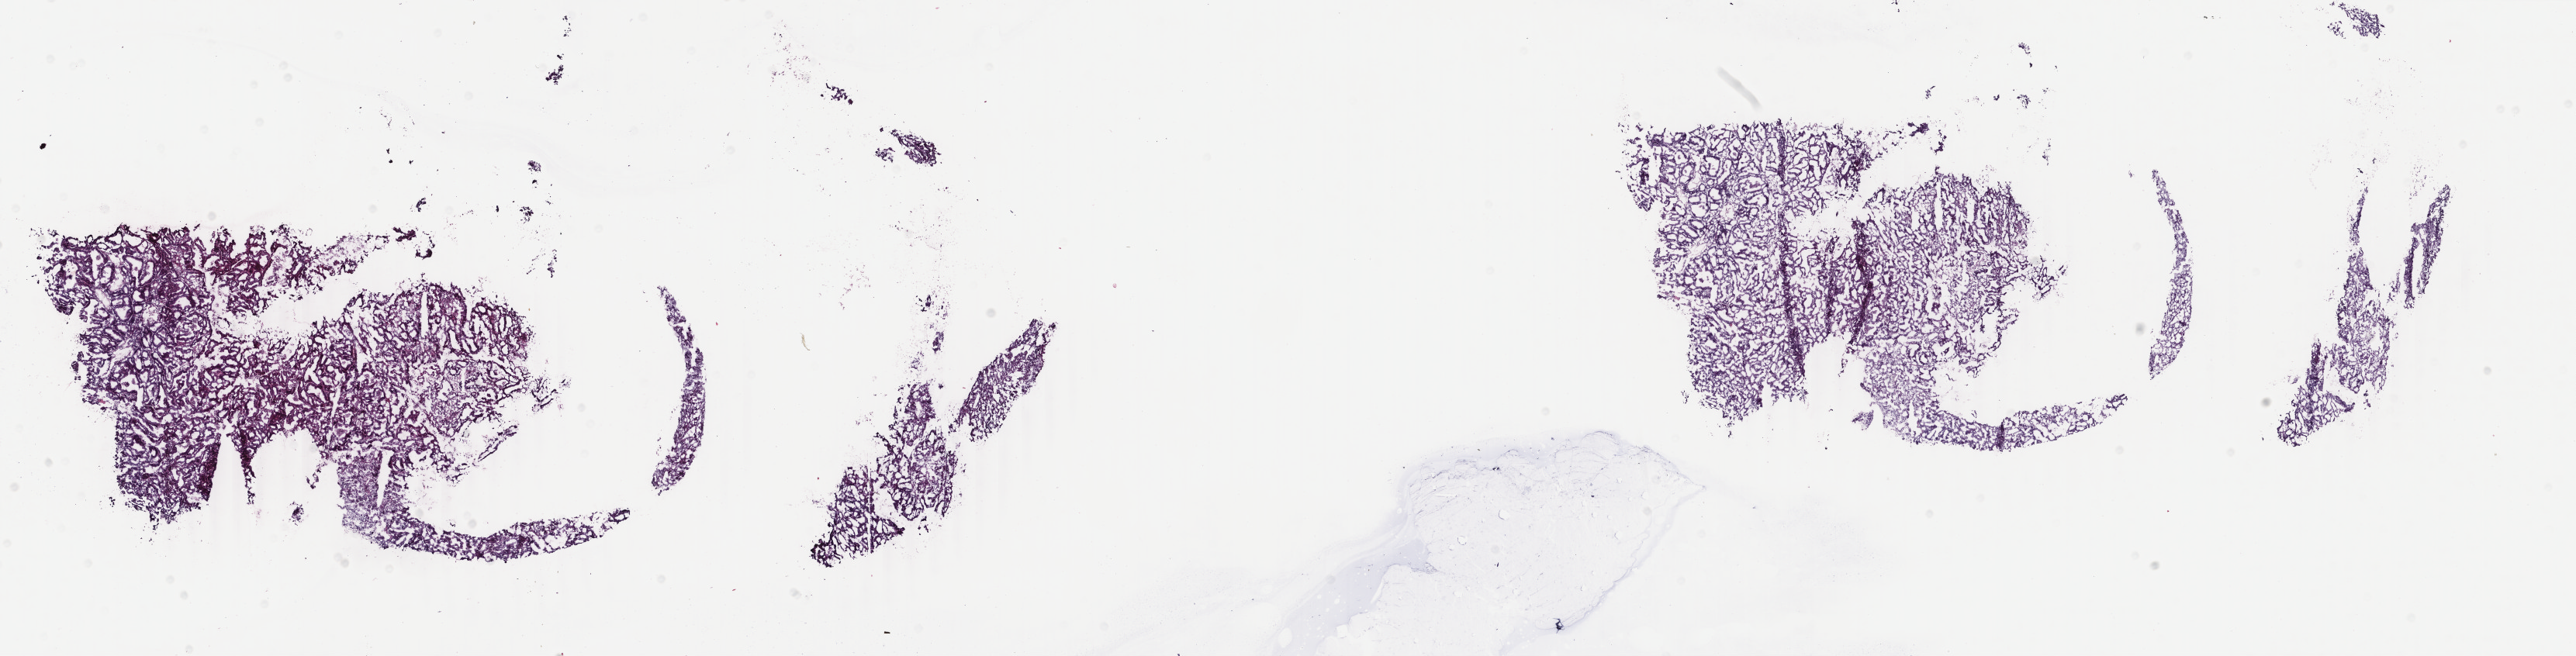
Digitized Hematoxylin and eosin (H&E) stained tissue section (whole slide) — shown as a low-resolution overview of the whole scanned area (about 26.4 x 6.7 mm, from a 40x scan). Frozen section from the top of the tissue portion. Uterus, primary tumour sample. Female patient; age at initial diagnosis 77 years. Slide review estimates, as recorded: tumour cells 60%, tumour nuclei 60%.
Pathologic diagnosis: Endometrioid adenocarcinoma, NOS (endometrium).